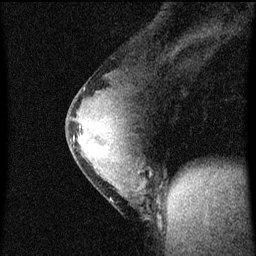
Breast MRI (dynamic contrast-enhanced), one sagittal slice. Slice 33 of 60 in the series (ordered by position). Dynamic contrast-enhanced series, image 2 of 4 at this slice position (ordered by acquisition). 1.5 T. TE 4.2 ms, TR 8 ms. 2 mm slice thickness. 256 × 256 image matrix. Female patient, age 33 years.
Structures marked on this image (semi-automatic segmentation, software-assisted and operator-edited):
- analysis volume of interest (the breast-tissue region the enhancement analysis was run in; not a lesion): bounding box (x1, y1, x2, y2) in pixels: (67, 76, 159, 219)
- tumour enhancement mask (voxels above the 70 % enhancement threshold inside the analysis volume of interest): (73, 122, 140, 173)